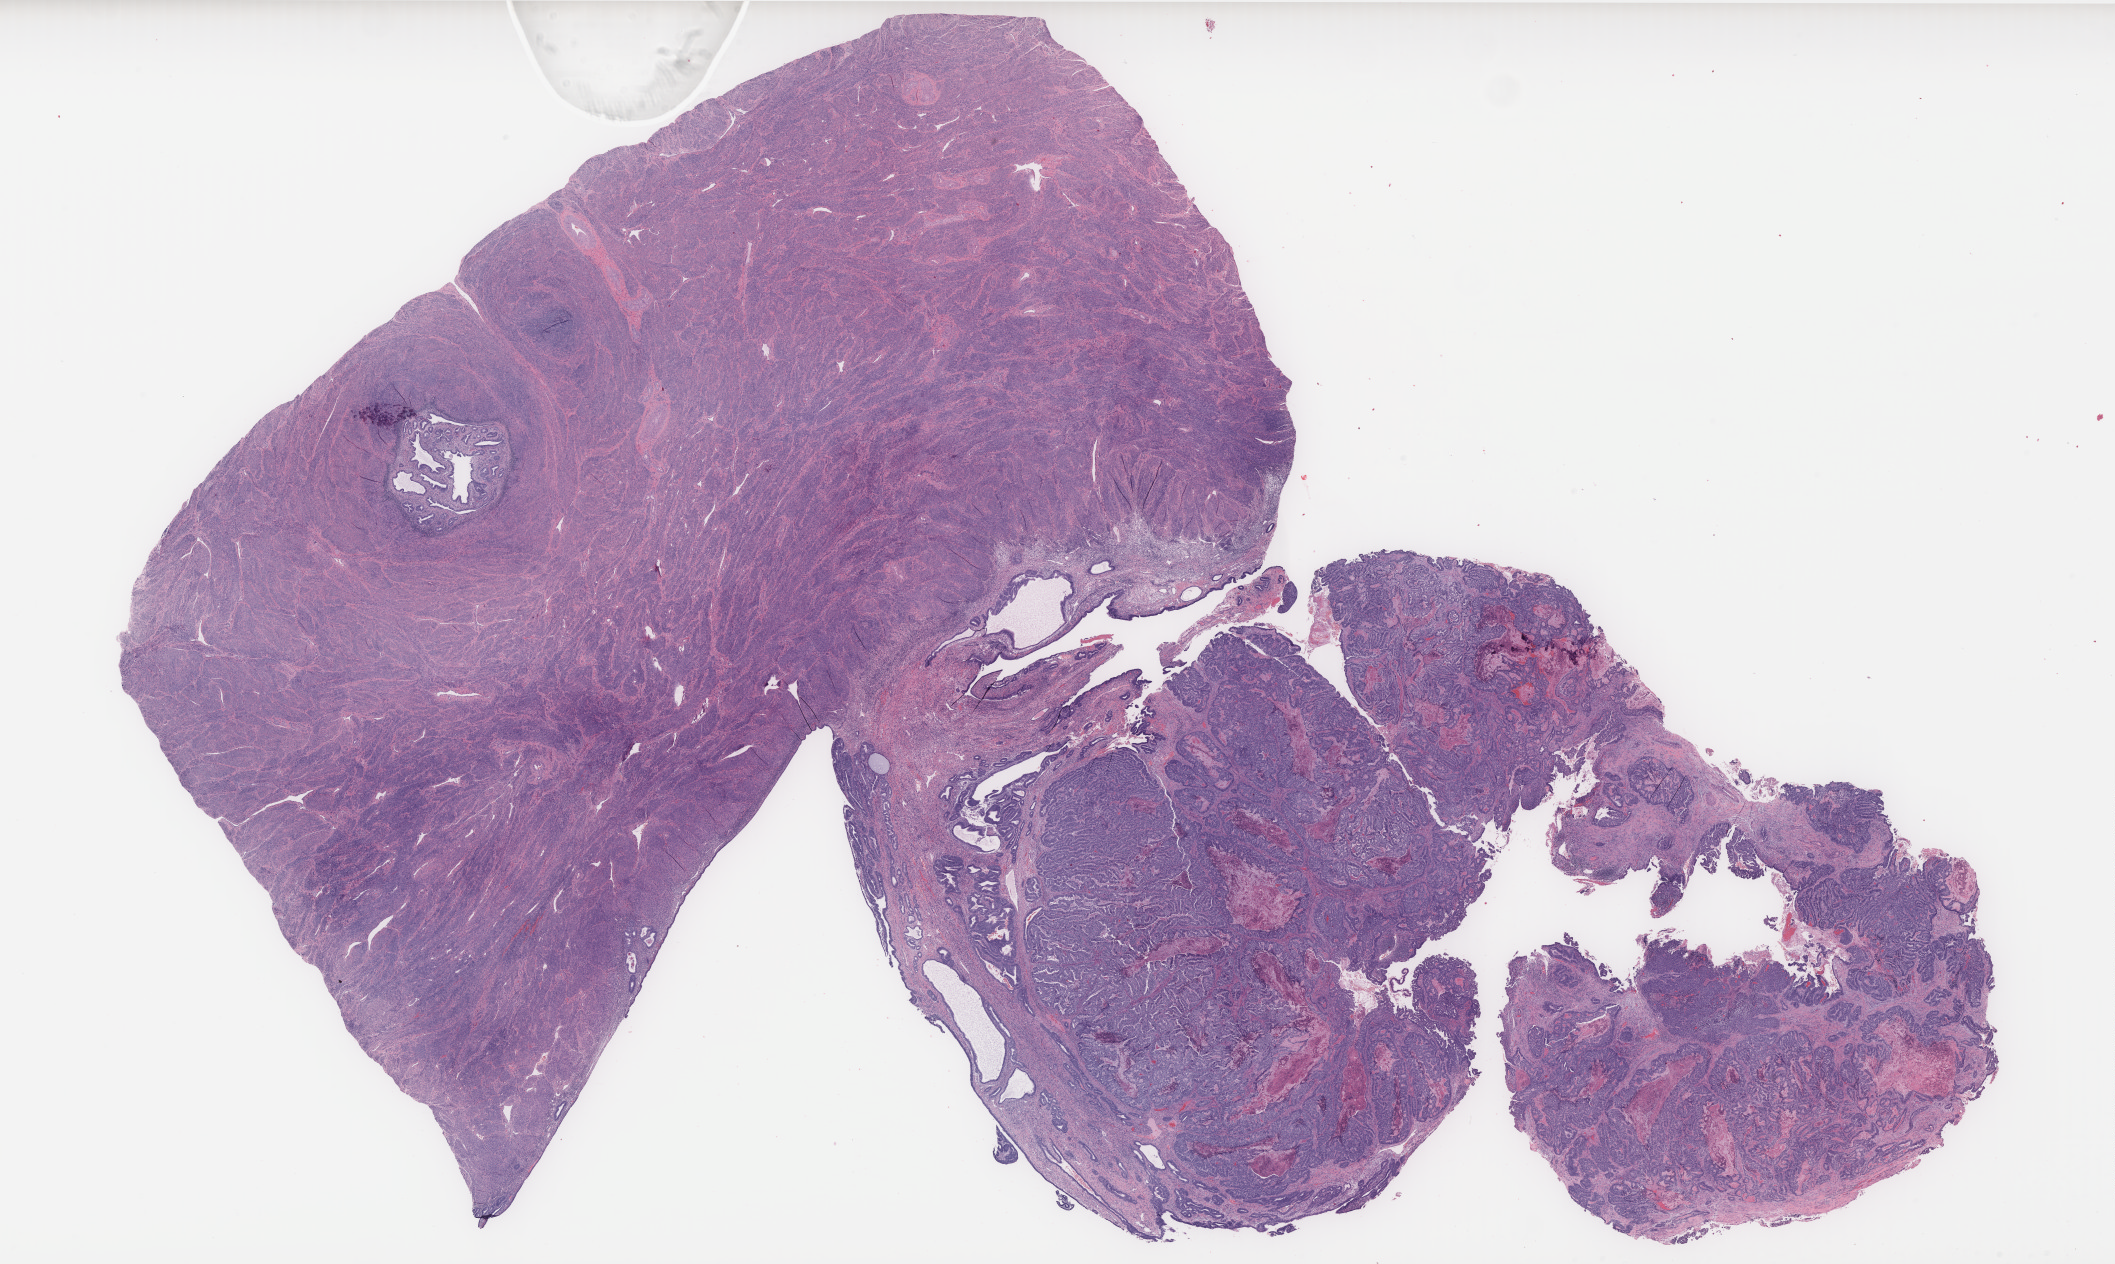
Whole-slide histology image, Hematoxylin and eosin (H&E) stained, whole scanned area (about 33.9 x 20.3 mm) shown as a low-resolution overview, formalin-fixed paraffin-embedded (FFPE) diagnostic section, uterus, primary tumour sample. Female, age 60 years at initial diagnosis.
Diagnosis: Endometrioid adenocarcinoma, NOS (endometrium).